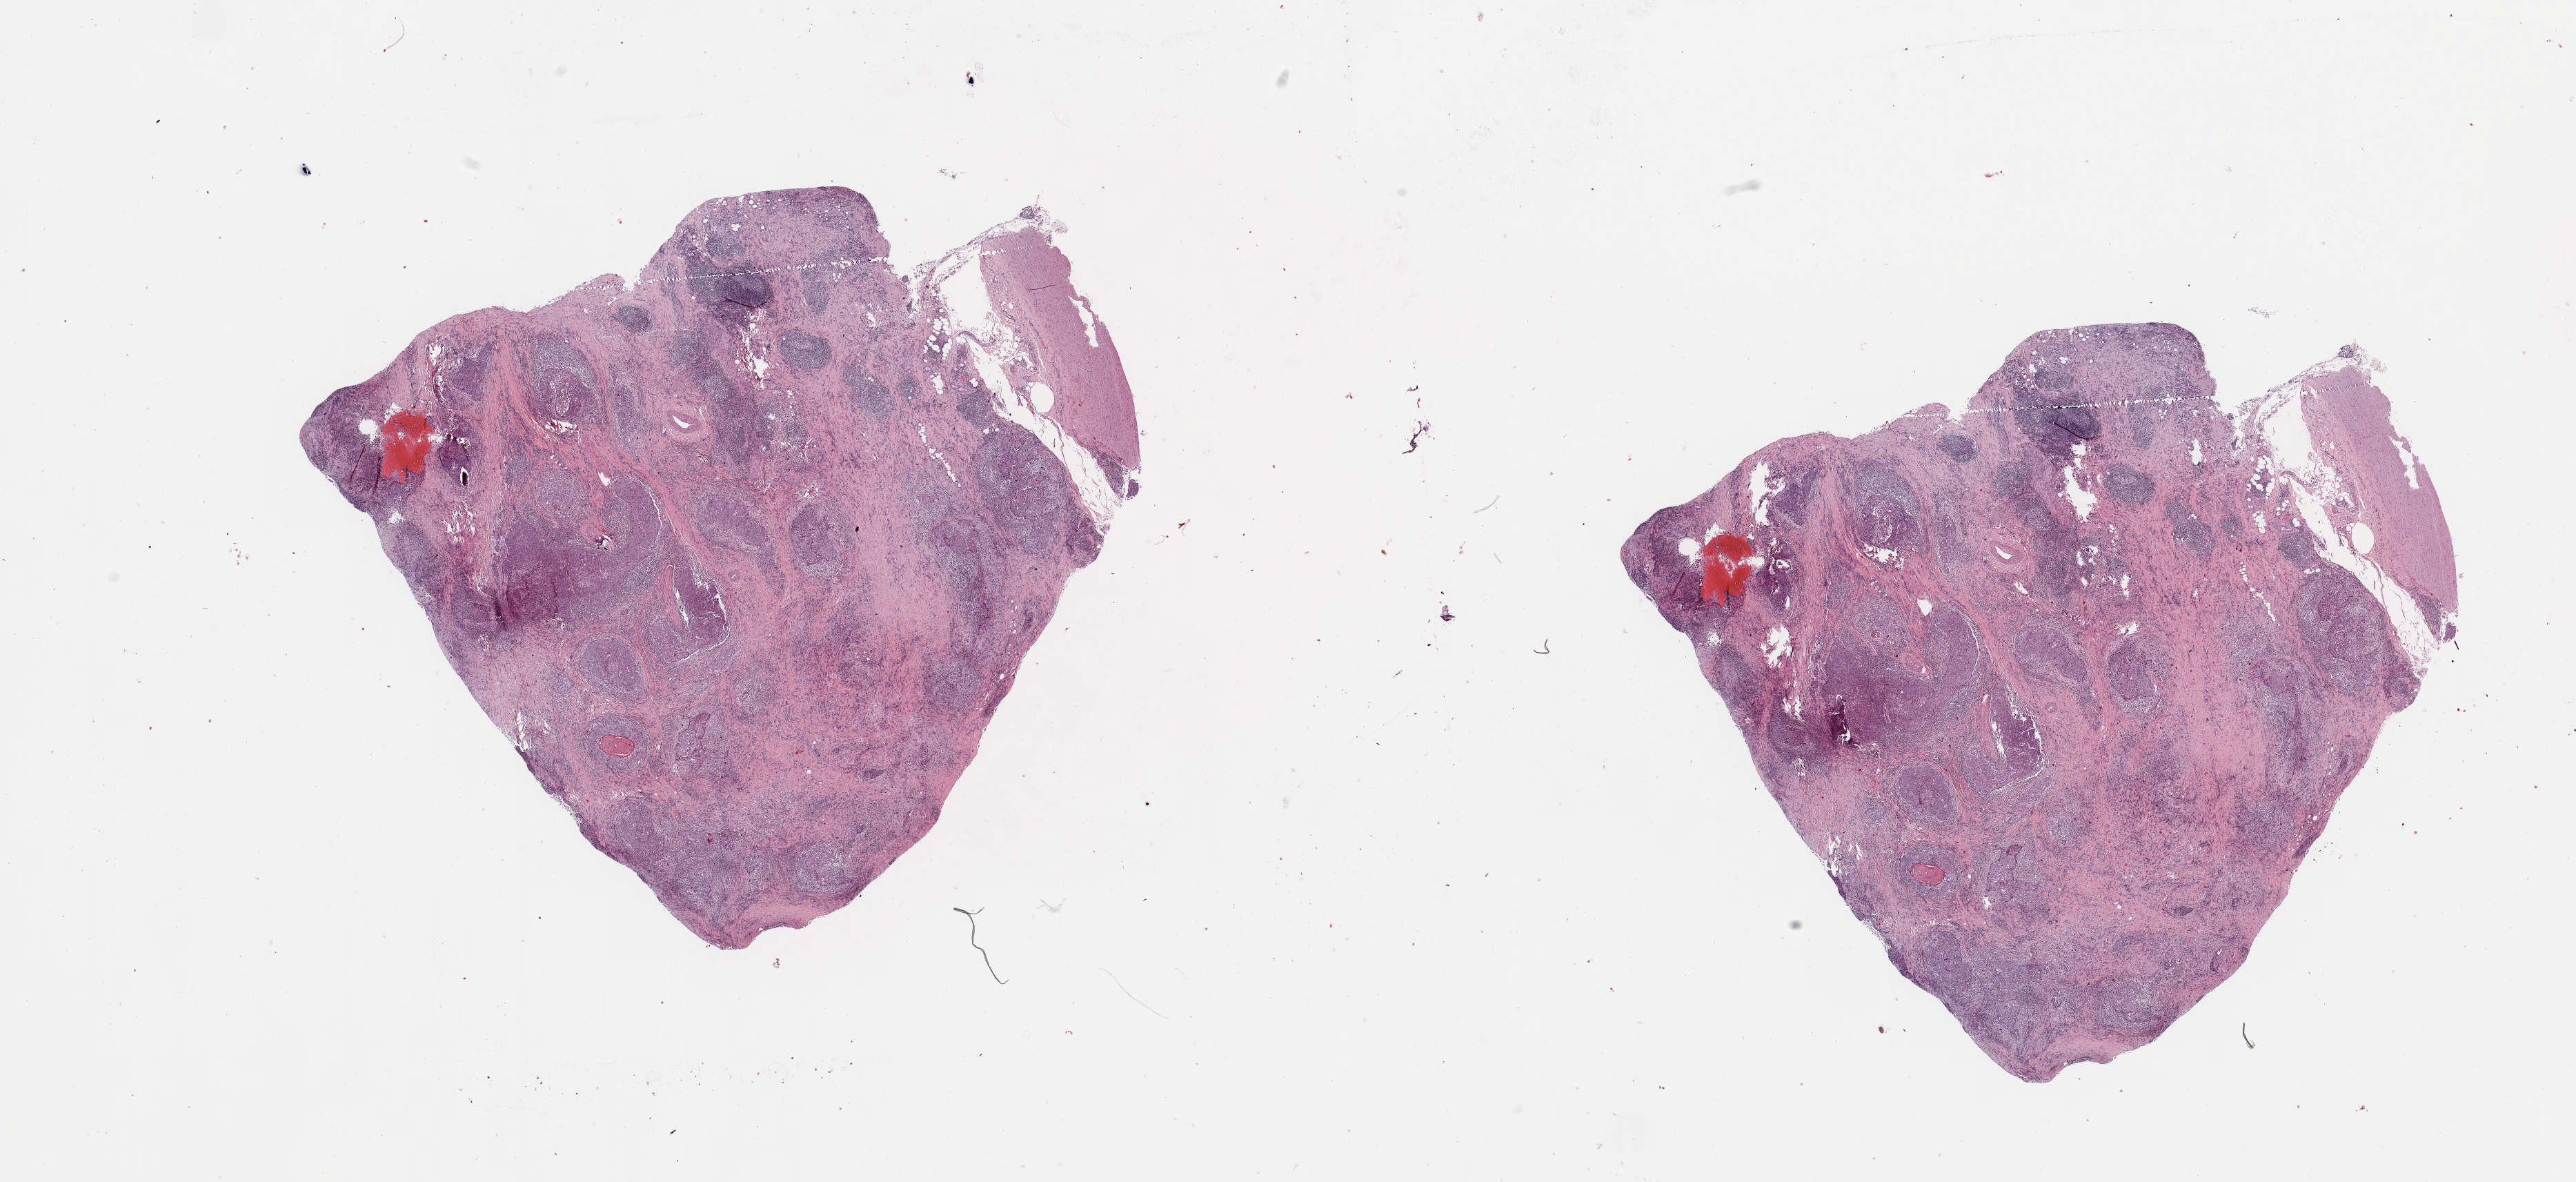
H&E whole-slide image, a low-resolution overview of the entire scanned area, about 29.5 x 13.5 mm. Lung, tumour tissue. 66-year-old male patient. Histologic grade: G3 (poorly differentiated).
- AJCC pathologic stage: IIA
- histologic diagnosis: Squamous cell carcinoma, NOS